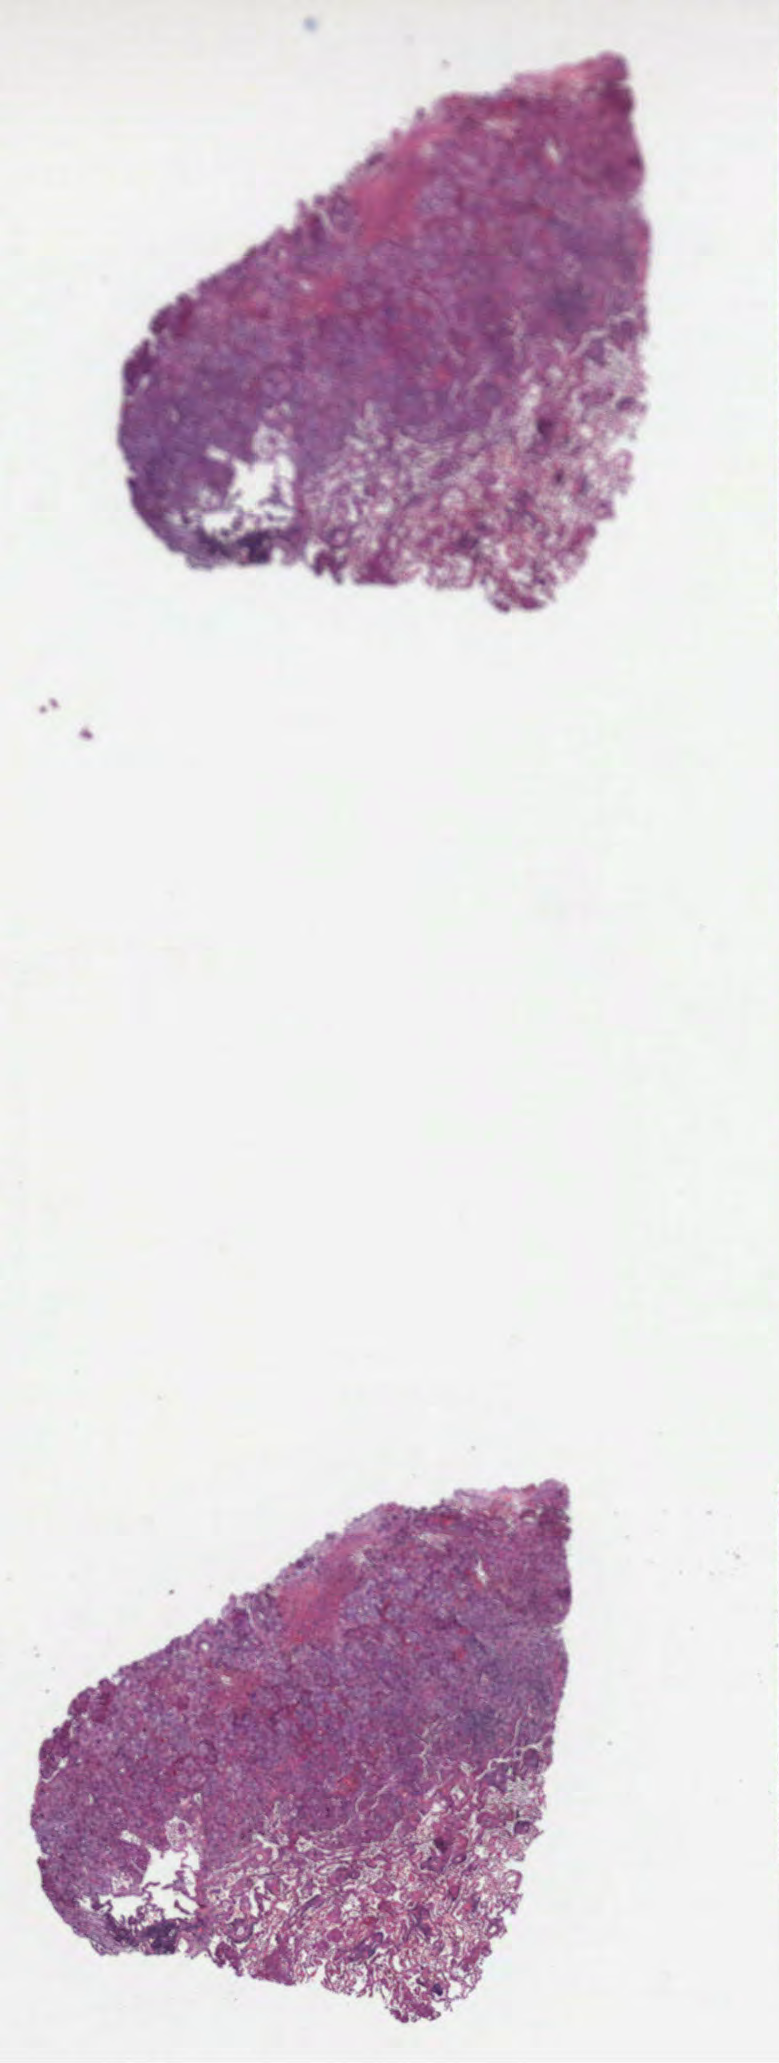
H&E whole-slide image, shown as a low-resolution overview of the whole scanned area (about 6.3 x 16.6 mm), formalin-fixed paraffin-embedded (FFPE) diagnostic section, primary tumour sample from the lung. Female patient; age at initial diagnosis 69 years.
Histologic diagnosis: Adenocarcinoma, NOS (lower lobe, lung).